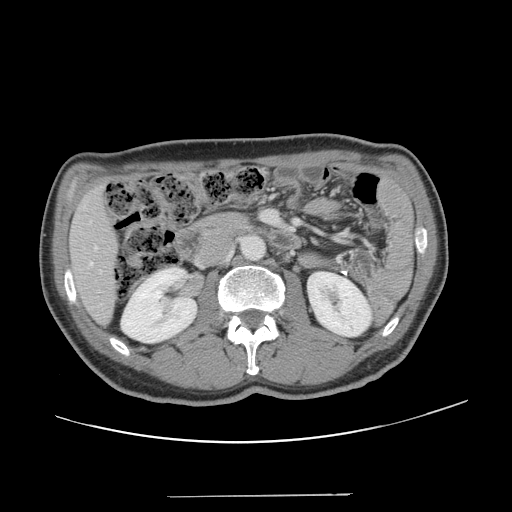
Contrast-enhanced abdominal CT, one axial slice; position 56 of 131 along the scan axis; soft-tissue window (W 400 / L 40 HU); 2.5 mm slice thickness; 512 × 512 image matrix. Male patient, age 60 years. Case-level facts recorded for this patient, not image findings: diagnosis: colorectal cancer liver metastases, imaged before liver resection; multiple liver metastases: no; largest metastasis: 2.5 cm.
Structures marked on this image (expert manual segmentation):
- hepatic veins: bounding box (x1, y1, x2, y2) in pixels: (90, 246, 97, 265)
- liver: (70, 191, 116, 322)
- planned liver remnant (the part of the liver to remain after resection): (70, 191, 116, 322)